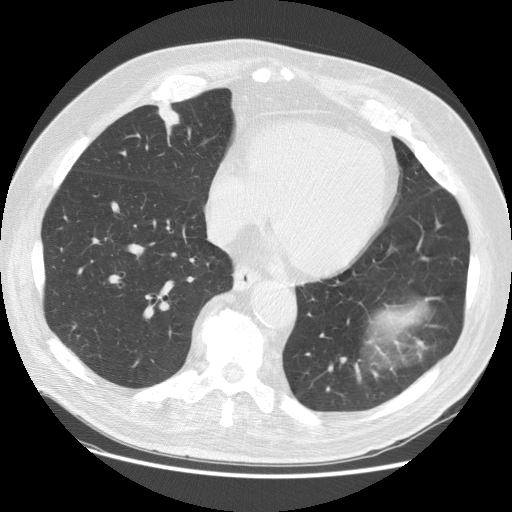
Low-dose screening chest CT, one axial slice. Position 40 of 129 along the scan axis. Lung window (W 1500 / L -600 HU). 2.5 mm slice thickness. 512 × 512 image matrix.
Outlined on this slice (manually delineated by an expert):
- lesion 1 (tumor, upper lobe of right lung): box from (x=158, y=104) to (x=180, y=125) px